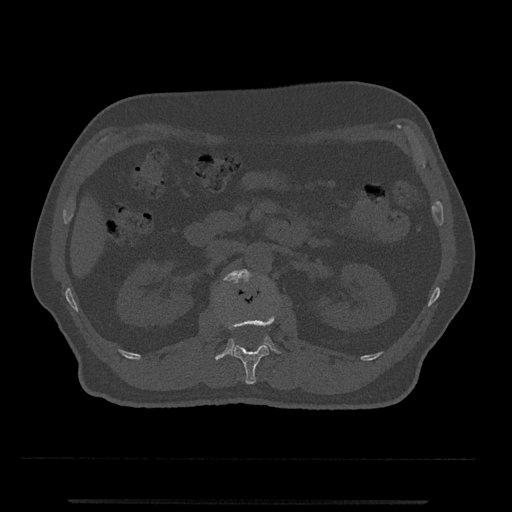
CT including the spine, one axial slice. 120 kVp. Bone window (W 1800 / L 400 HU). 0.5 mm slice thickness. 512 × 512 image matrix. Male patient, age 63 years. Case-level facts recorded for this patient, not image findings: primary cancer: prostate.
Structures marked on this image (semi-automatic segmentation, software-assisted and operator-edited):
- L1 vertebra: bounding box [x1, y1, x2, y2] px = [225, 312, 275, 384]
- L2 vertebra: [215, 269, 281, 361]